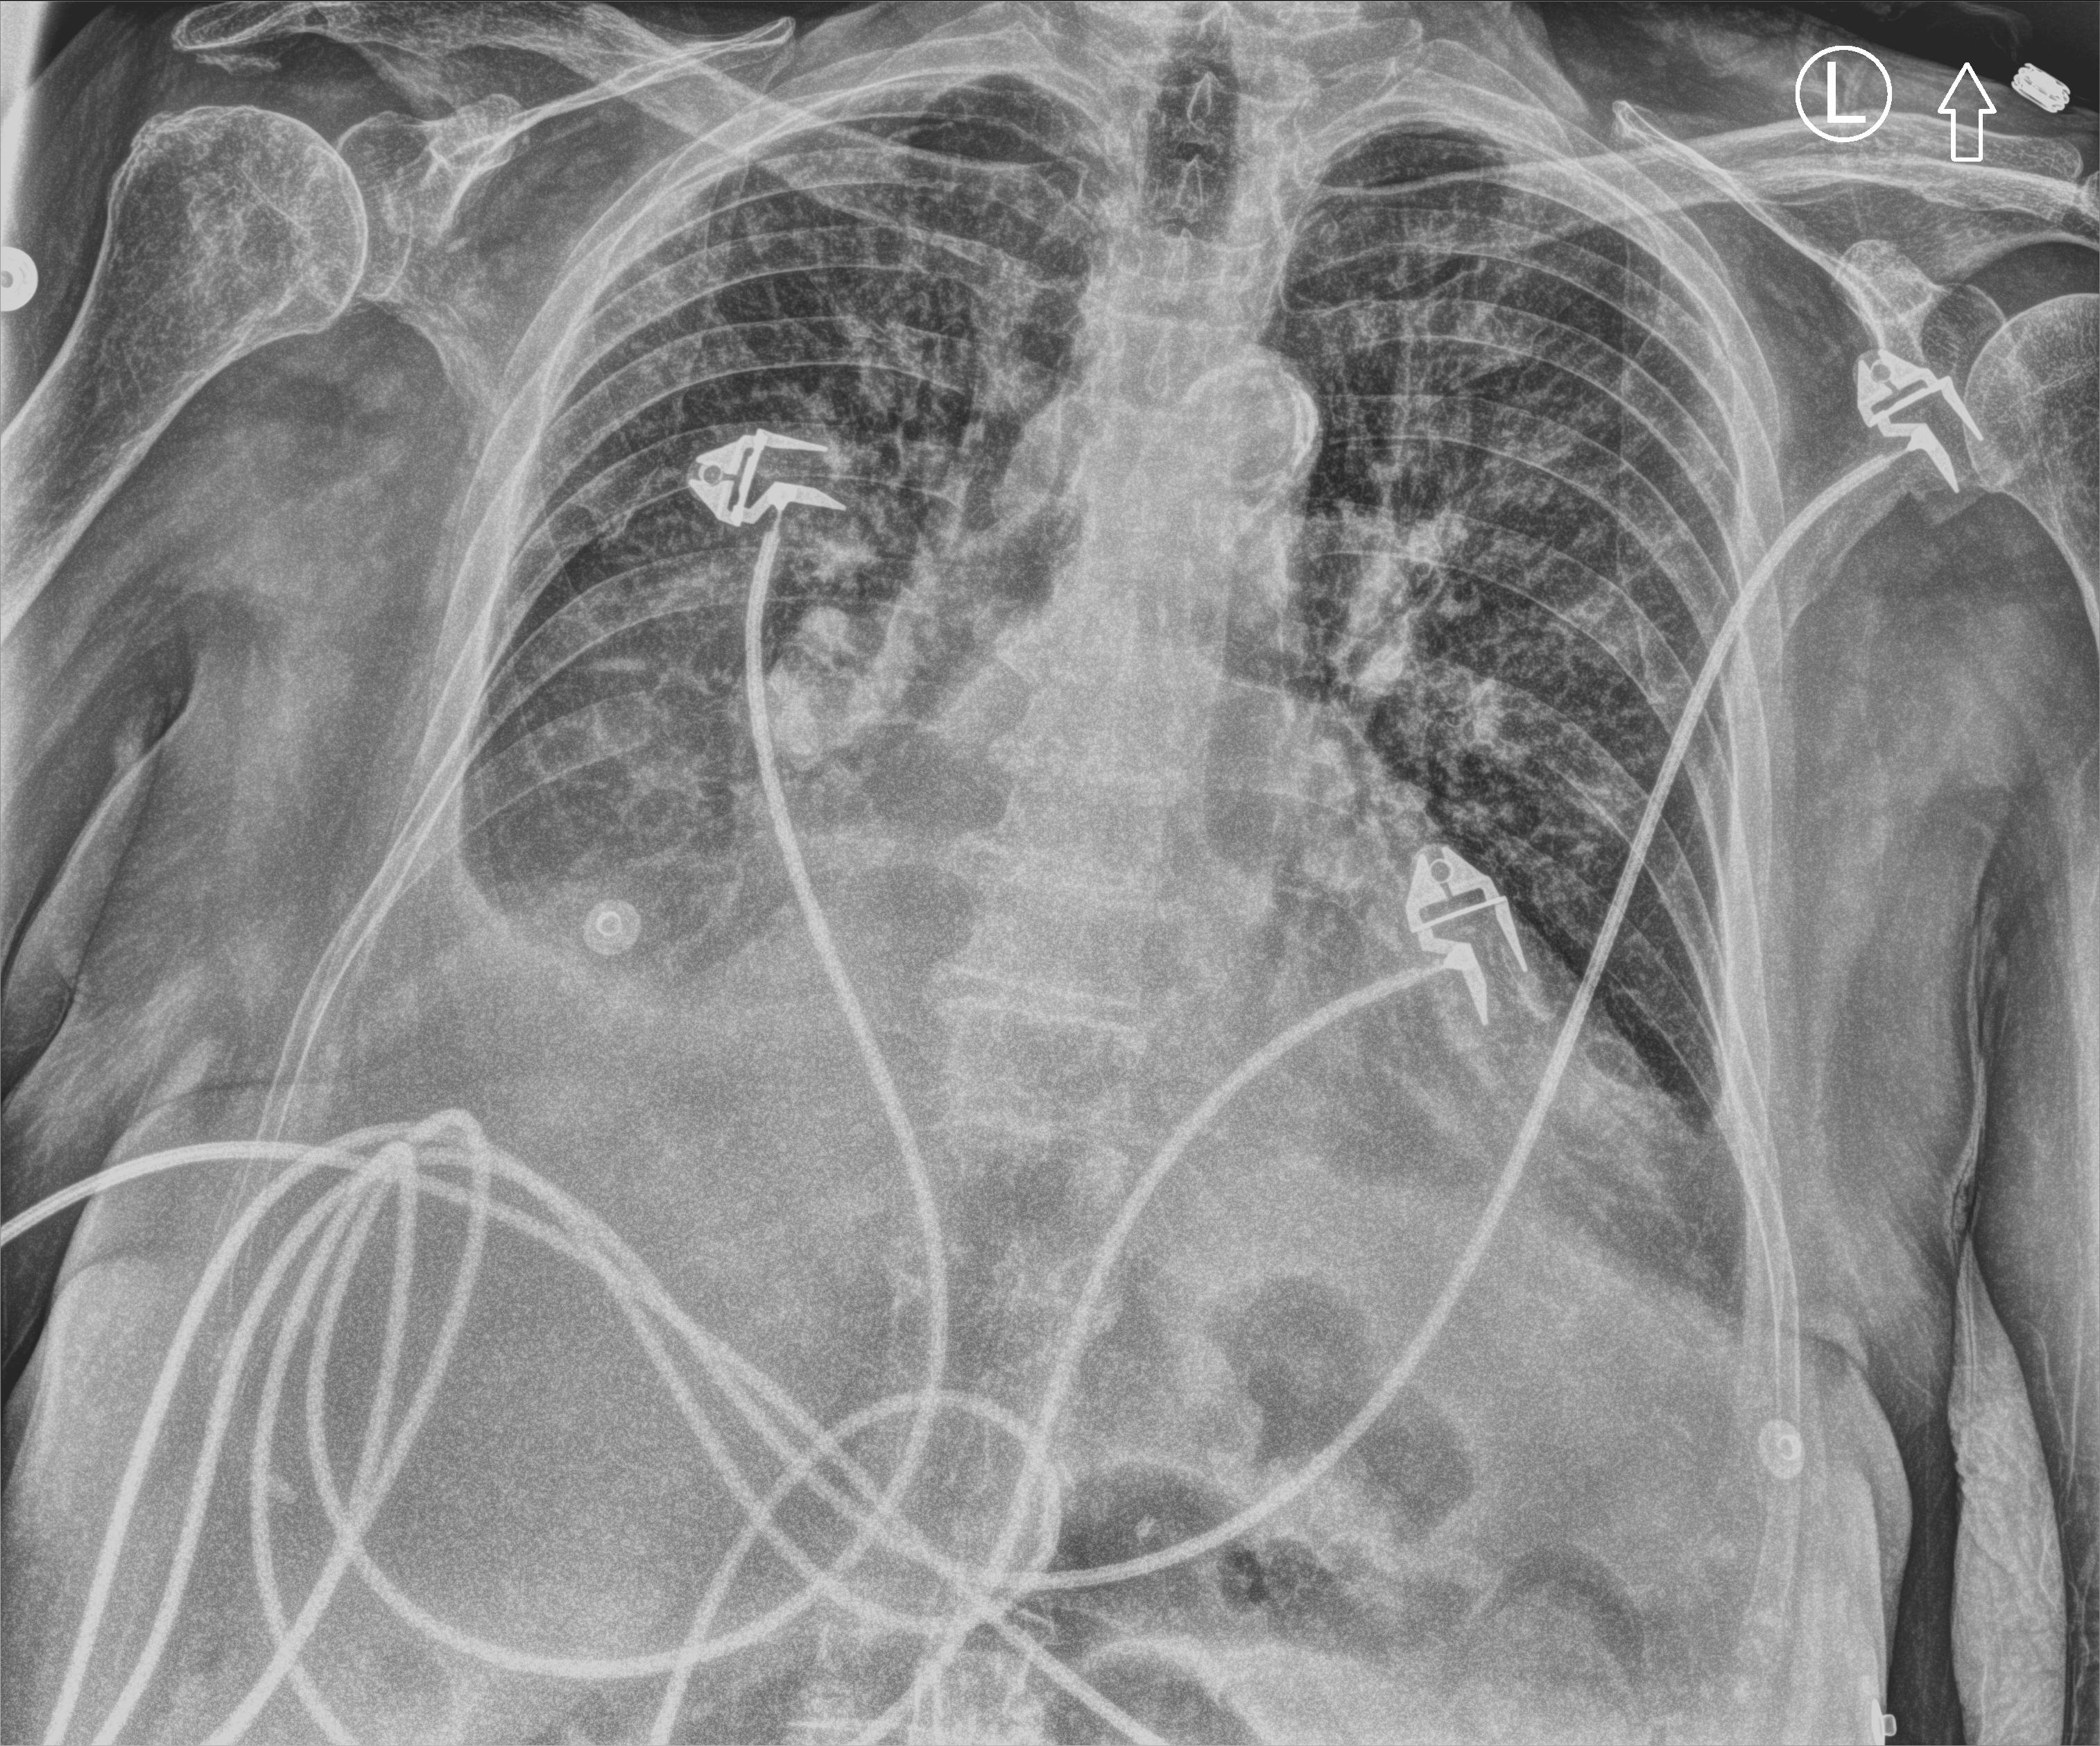
Chest X-ray (portable), anteroposterior (AP) projection. Patient hospitalised with COVID-19; female, aged 75–90 years.
Hospital-stay facts (about this admission, not read from this image; timing relative to this image not recorded): admitted to intensive care during this hospital stay: yes.